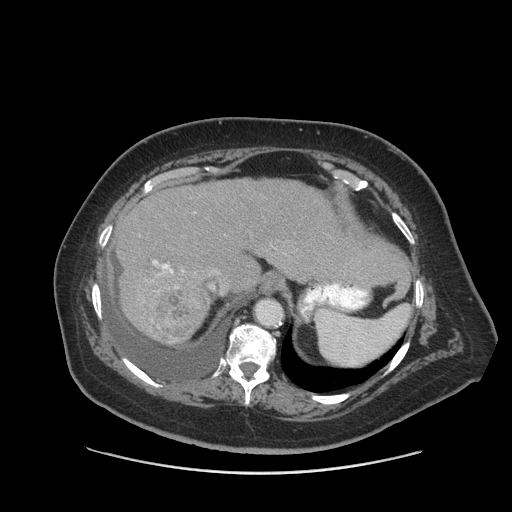
Contrast-enhanced abdominal CT (liver protocol), one axial slice. Position 65 of 91 along the scan axis. Reconstruction kernel STANDARD. Soft-tissue window (W 400 / L 40 HU). 512 × 512 image matrix, field of view 420 × 420 mm. From the clinical record (not read from this slice): diagnosis: hepatocellular carcinoma (patient treated with transarterial chemoembolisation; whether this scan precedes or follows treatment is not stated here); TNM stage (as recorded): Stage-I.
Outlined on this slice (semi-automatic segmentation, software-assisted and operator-edited):
- liver parenchyma outside the tumour (the mass and vessels are separate outlines, so this box may not span the whole liver): bounding box [x1, y1, x2, y2] px = [116, 178, 388, 344]
- mass: [151, 286, 210, 342]
- liver vessels: [153, 260, 173, 273]